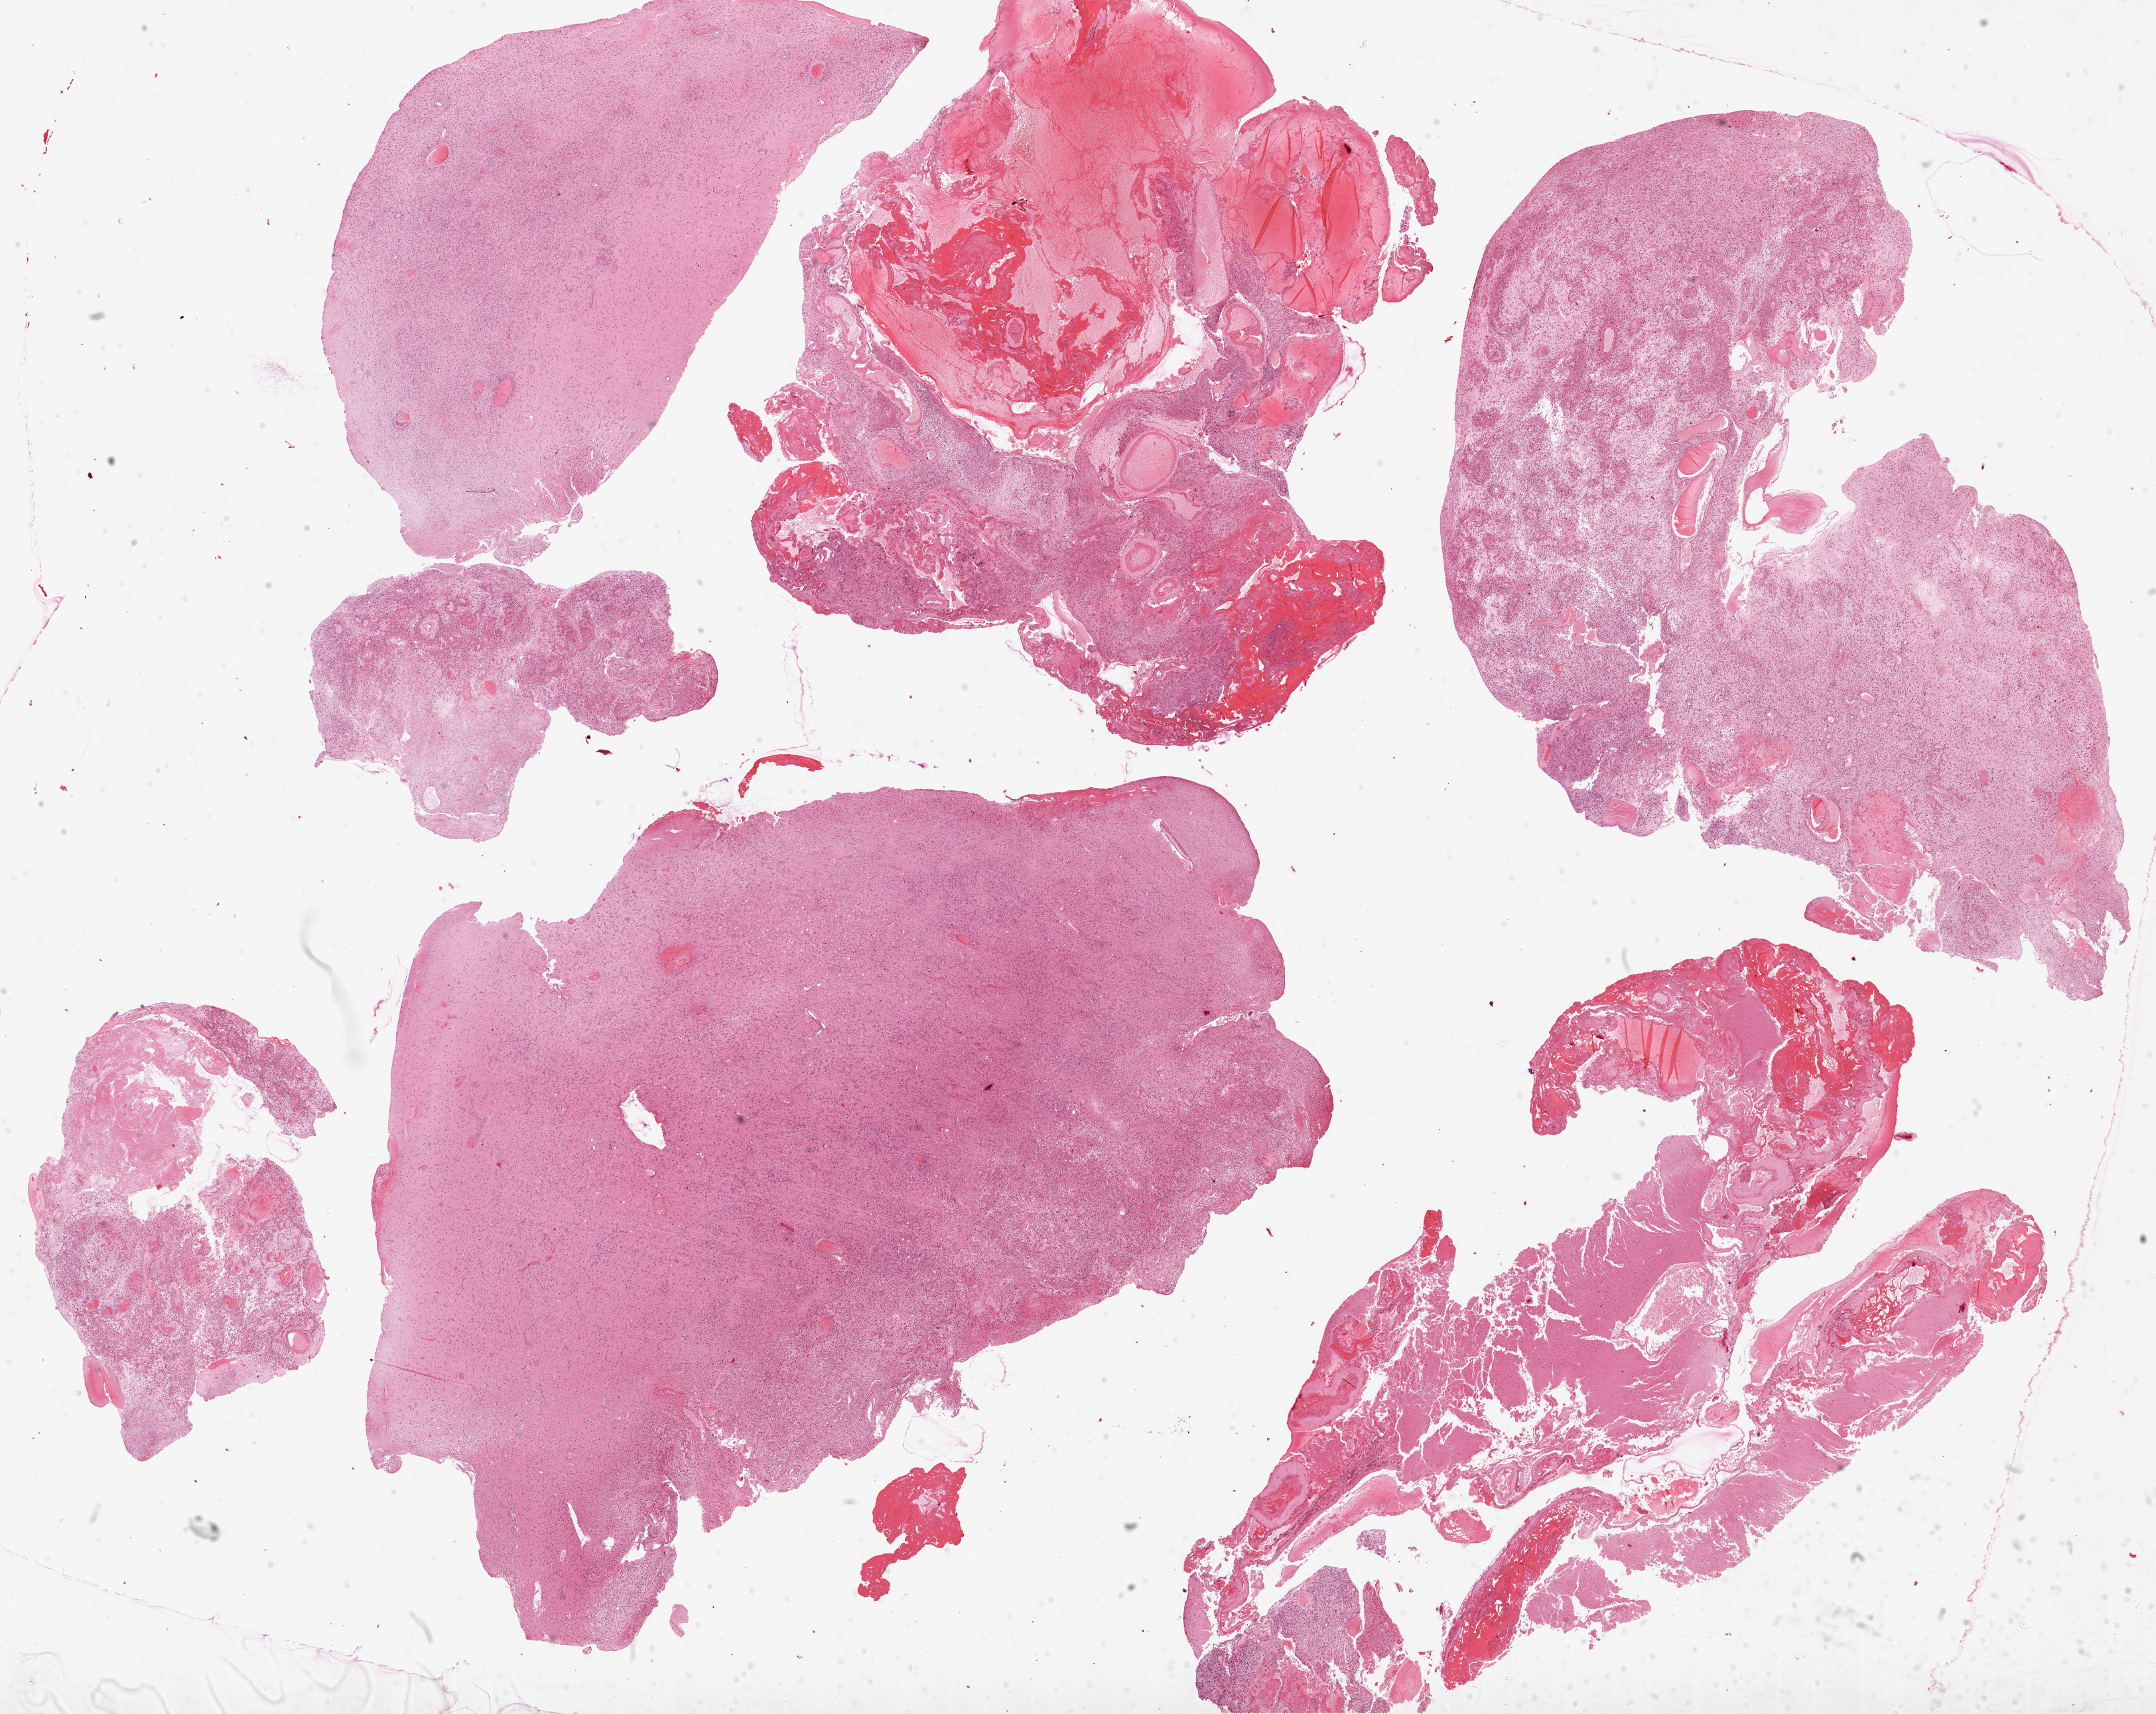
H&E whole-slide image — whole scanned area (about 26.1 x 20.7 mm) shown as a low-resolution overview, formalin-fixed paraffin-embedded (FFPE) diagnostic section, sample: primary tumour, brain. Male, age 57 years at initial diagnosis.
Pathologic diagnosis: Glioblastoma.